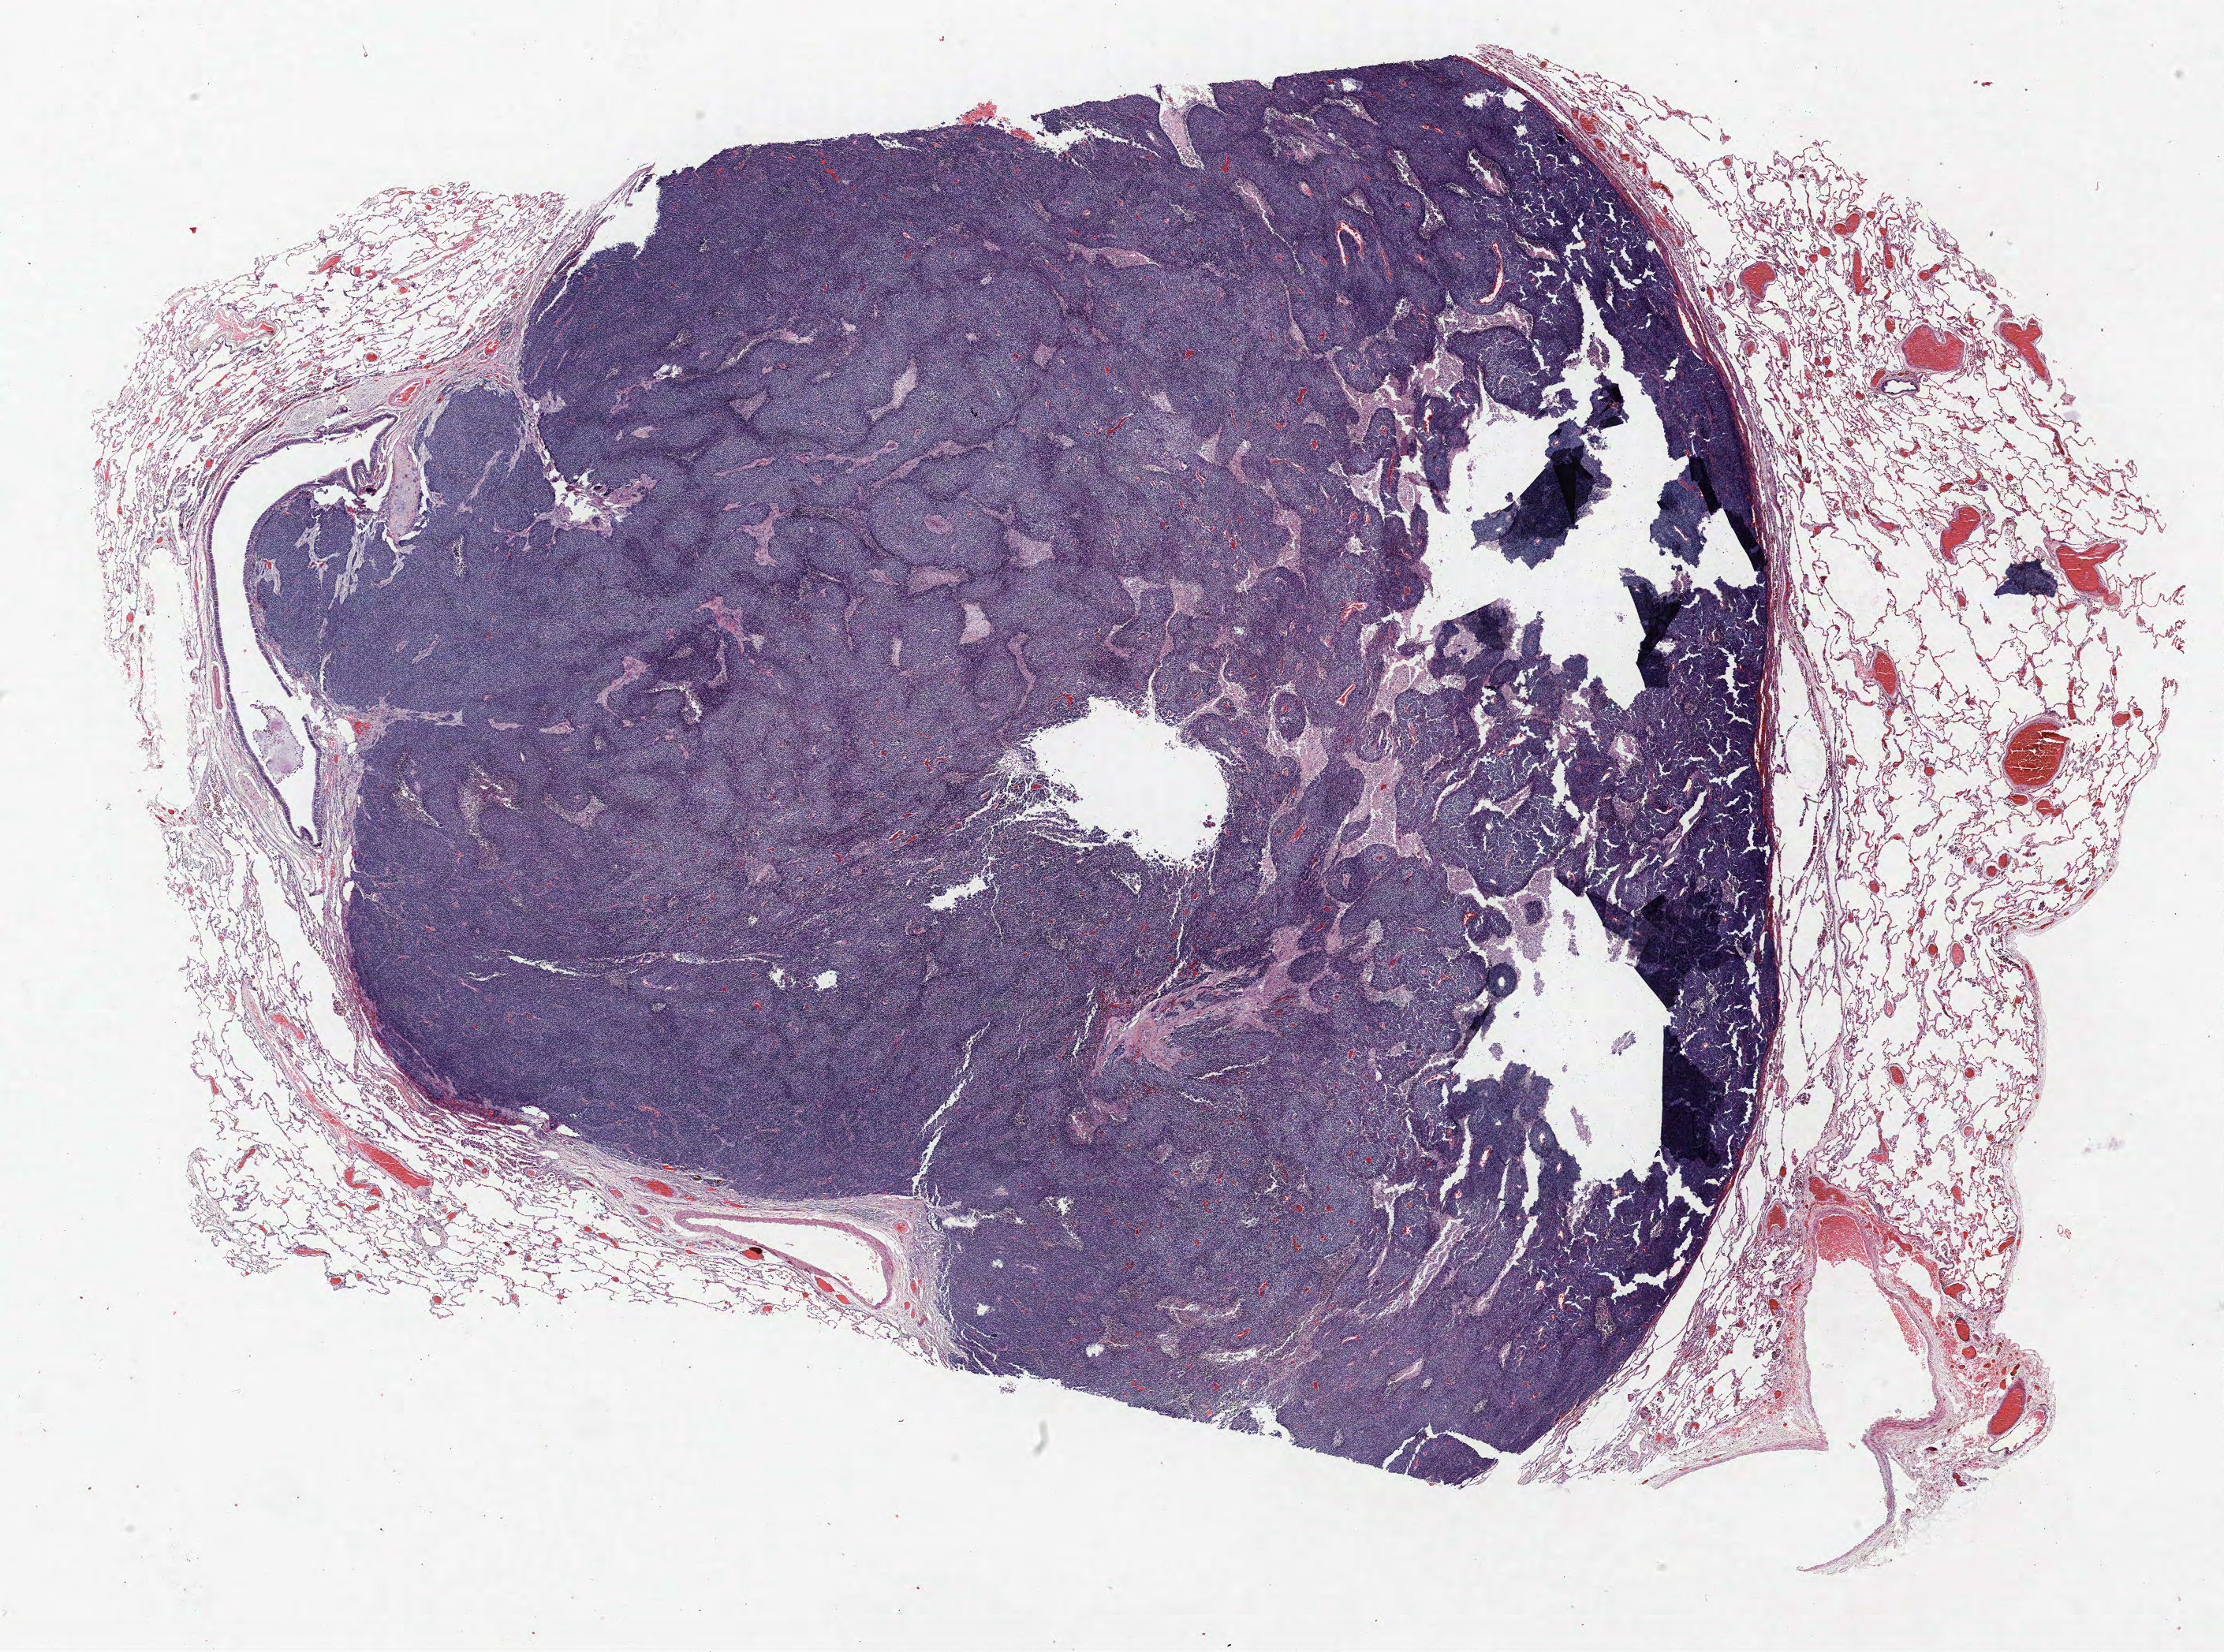
Hematoxylin and eosin (H&E) stained whole-slide image, a low-resolution overview of the entire scanned area, about 22.6 x 16.8 mm (slide scanned at 40x). Formalin-fixed paraffin-embedded (FFPE) section. Lung. Male, age 64 at enrolment. Grade: poorly differentiated (G3).
Participant's lung-cancer diagnosis: Non-small cell carcinoma. Stage (AJCC 6th edition): IIIA. Tumour size (pathology): 20 mm. Primary tumour location (clinical record): right middle lobe.